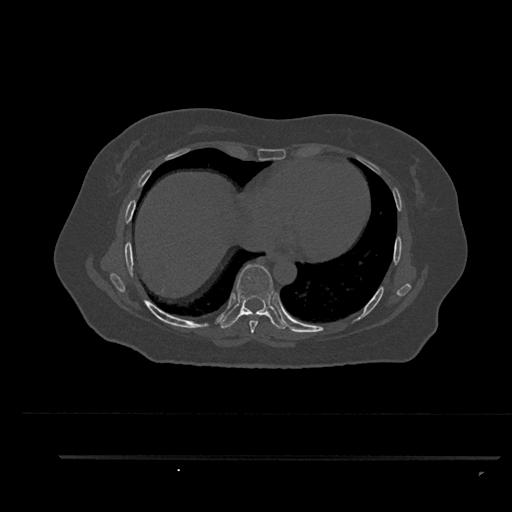
CT including the spine, one axial slice; slice 475 of 797 in the series (ordered by position); reconstruction kernel Br40s/3; bone window (W 1800 / L 400 HU); 0.5 mm slice thickness; 512 × 512 image matrix. Female patient, age 44 years. From the clinical record (not read from this slice): primary cancer: renal.
Outlined on this slice (semi-automatically segmented with operator editing):
- T7 vertebra: box from (x=249, y=320) to (x=258, y=333) px
- T8 vertebra: (x=220, y=264)–(x=287, y=329)